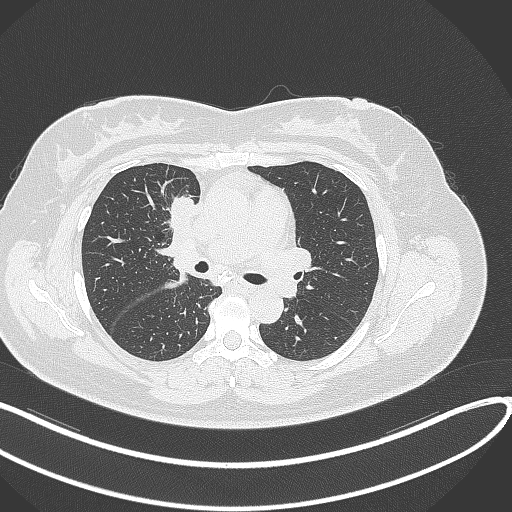
Chest CT, one axial slice. Slice 164 of 303 in the series (ordered by position). Reconstruction kernel B70f. 120 kVp. Lung window (W 1500 / L -600 HU). 512 × 512 image matrix. Female patient, age 46 years. Case-level facts recorded for this patient, not image findings: clinical TNM (as recorded): T2a N1 M0.
Annotated regions visible in this slice (bounding box drawn by a radiologist):
- lung tumour (recorded histology: adenocarcinoma): bounding box (x1, y1, x2, y2) in pixels: (168, 196, 196, 229)